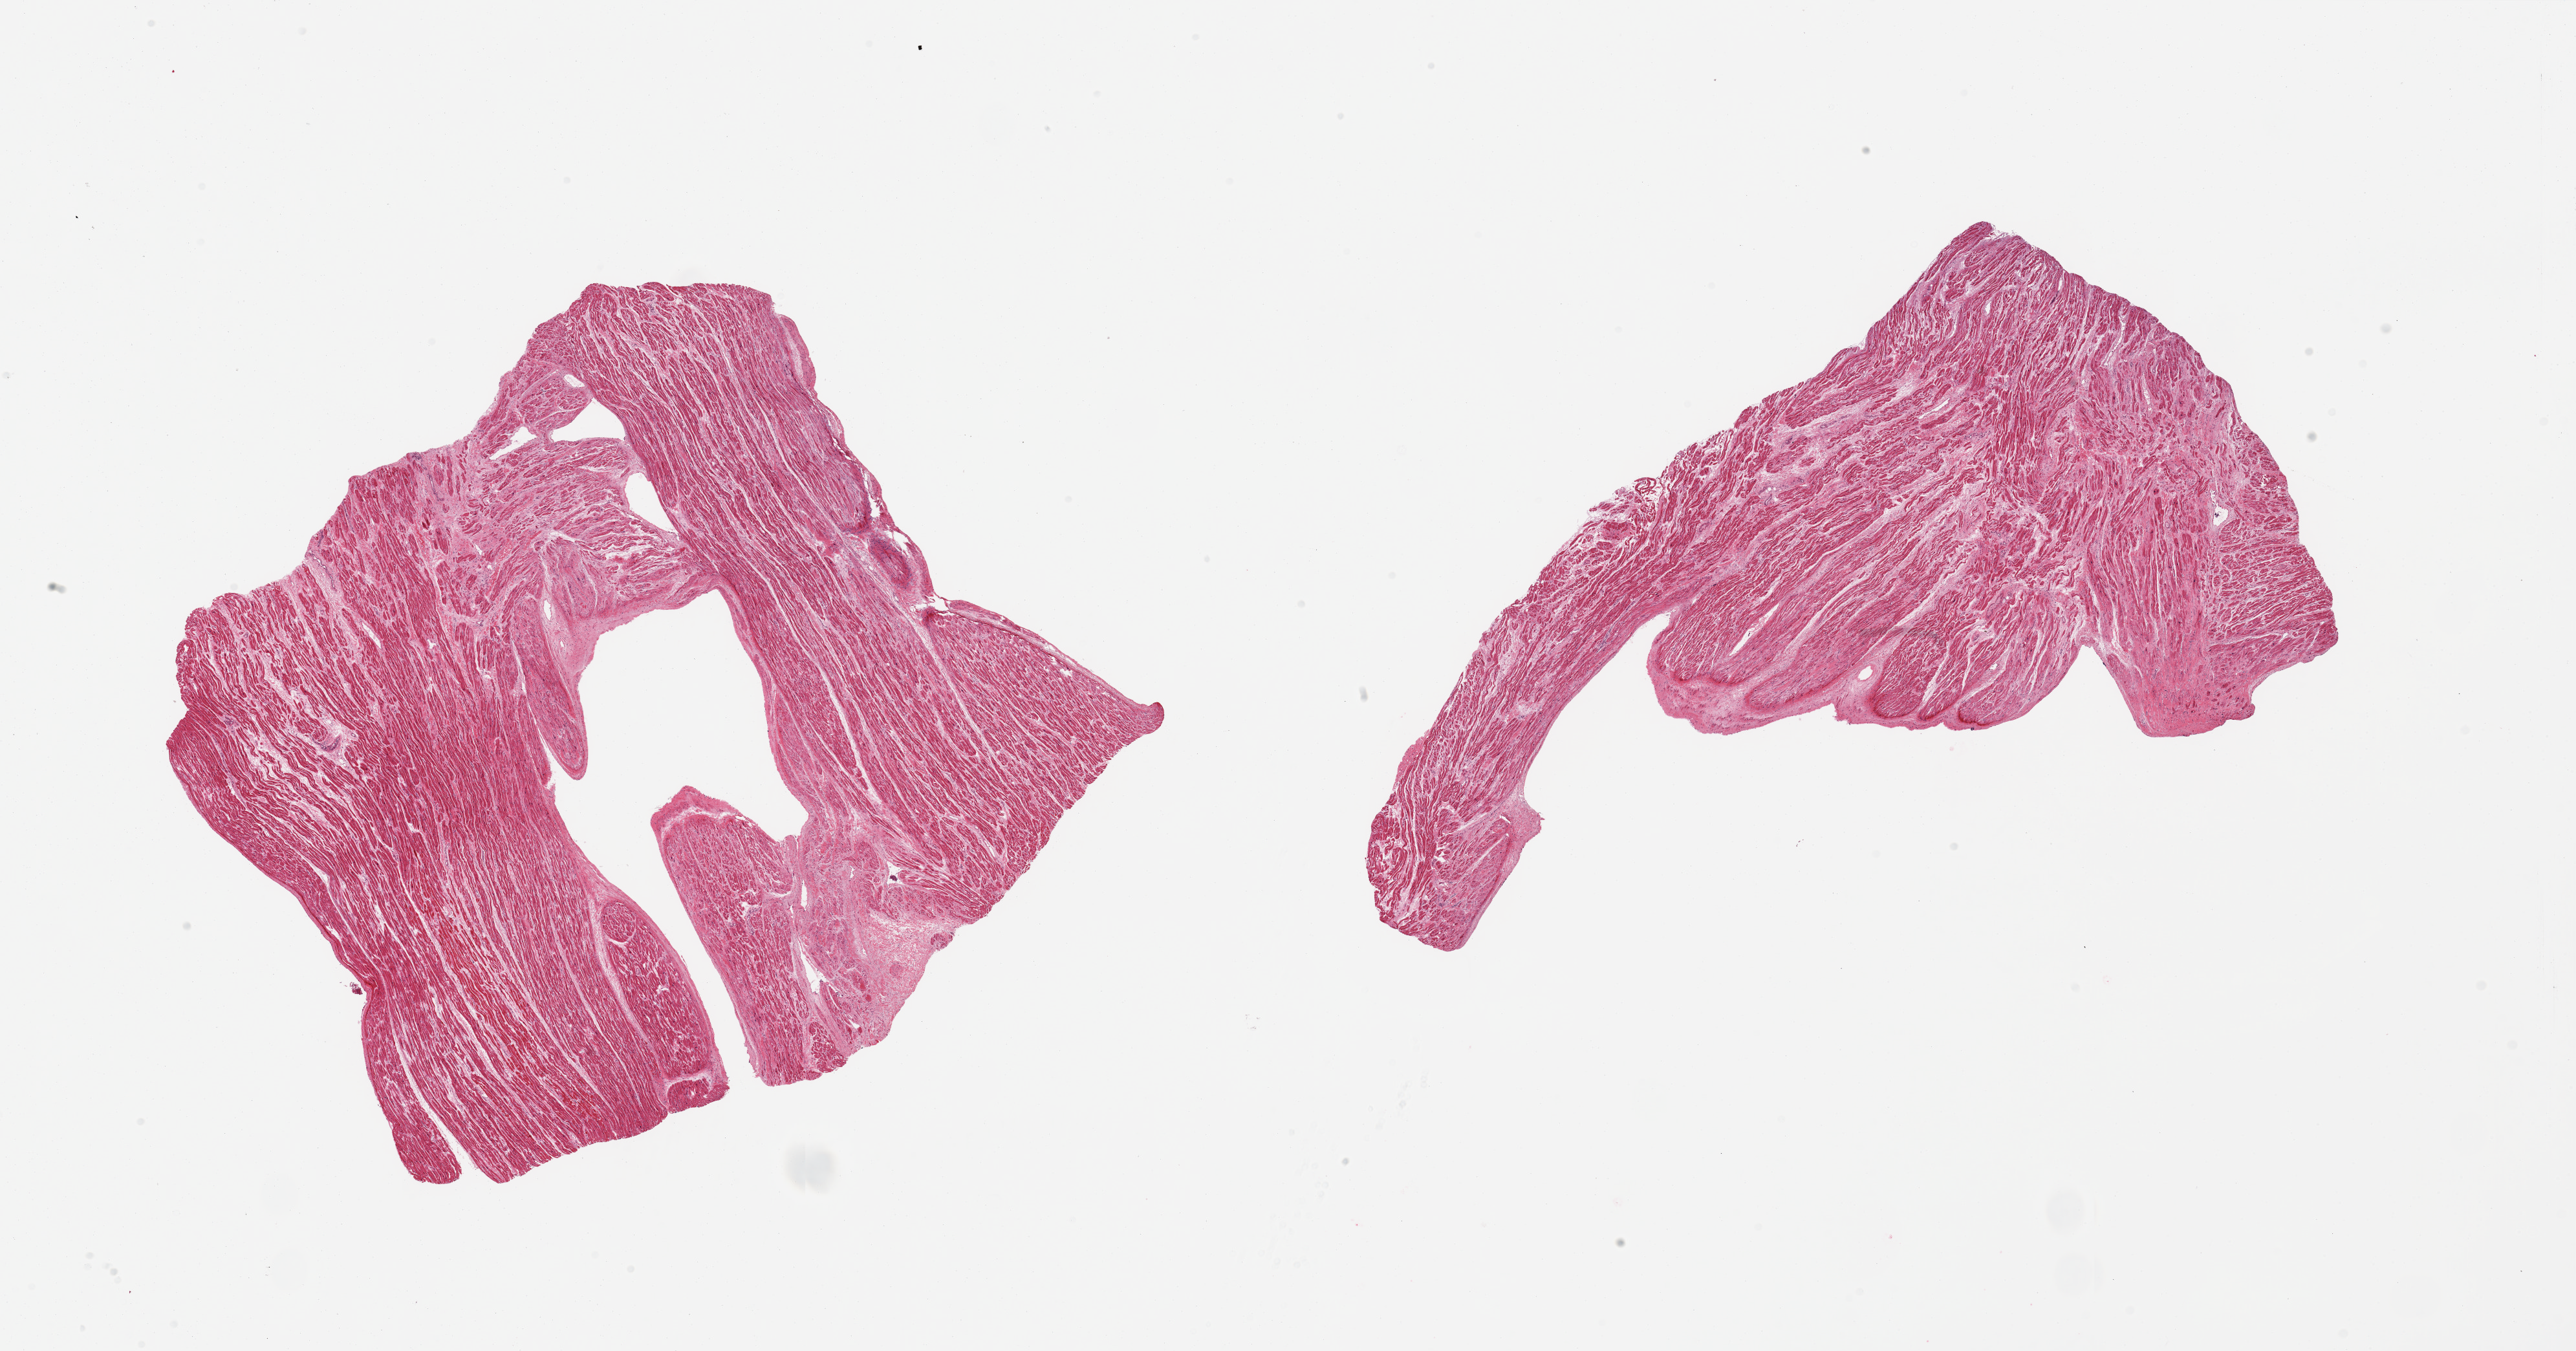
Whole-slide image, H&E stain, brightfield, low-resolution overview of the scanned area, about 31.5 x 16.5 mm; PAXgene-fixed paraffin-embedded (PFPE) section; sampled site (target tissue): auricular appendage; donor tissue sample. Male donor.
Review note (as recorded): 2 pieces, no abnormalities.